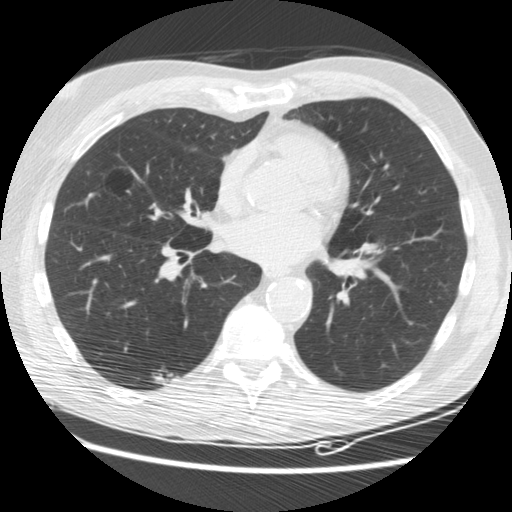
Axial slice from a low-dose chest CT screening exam; third annual screen; lung window (W 1500 / L -600 HU); standard (soft-tissue) reconstruction kernel (STANDARD). Male participant, aged 62 years at enrolment. Current smoker at enrolment.
Expert-annotated lung lesion, bounding box <143,361,178,395> (left, top, right, bottom; pixels). The screening reader recorded 3 non-calcified nodules or masses ≥4 mm on this exam (right lower lobe, right lower lobe, right lower lobe); which of them this box marks is not recorded. Later outcome: lung cancer diagnosed 33 days after this screen — adenocarcinoma, NOS, right lower lobe, moderately differentiated (G2), stage IIIB (AJCC 6th edition), 15 mm at pathology.